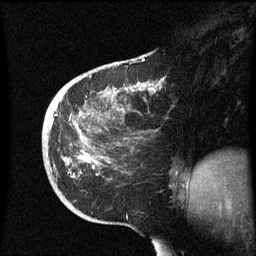
Breast MRI (dynamic contrast-enhanced), one sagittal slice; slice 22 of 60 in the series (ordered by position); dynamic contrast-enhanced series, image 2 of 3 at this slice position (ordered by acquisition); 1.5 T; TE 4.2 ms, TR 8.4 ms; 2.3 mm slice thickness; 256 × 256 image matrix. Patient: female, 38 years. Case-level facts recorded for this patient, not image findings: setting: breast cancer imaged before/during neoadjuvant chemotherapy; receptor status: HER2-positive.
Annotated regions visible in this slice (semi-automatic segmentation, software-assisted and operator-edited):
- analysis volume of interest (the breast-tissue region the enhancement analysis was run in; not a lesion): bounding box <42,78,191,213> (left, top, right, bottom; pixels)
- tumour enhancement mask (voxels above the 70 % enhancement threshold inside the analysis volume of interest): <52,84,153,163>